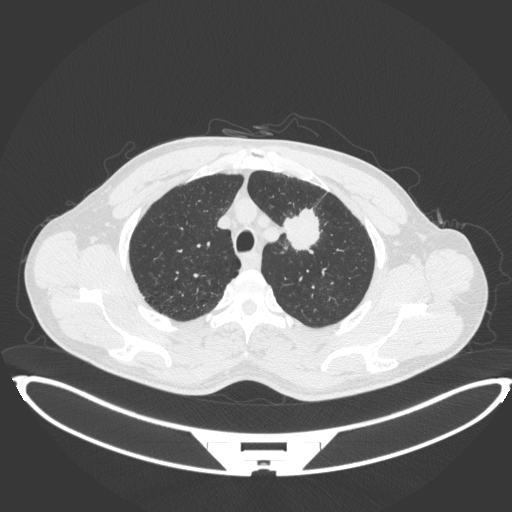
Chest CT, one axial slice; position 354 of 407 along the scan axis; reconstruction kernel B31f; lung window (W 1500 / L -600 HU); 1 mm slice thickness; 512 × 512 image matrix, field of view 457 × 457 mm. Male patient, age 60 years. Case-level facts recorded for this patient, not image findings: clinical TNM (as recorded): T2a N0 M0; histopathological grade: G1-G2.
Annotated regions visible in this slice (rectangle marked by the reading radiologist):
- lung tumour (recorded histology: squamous cell carcinoma): bounding box [x1, y1, x2, y2] px = [279, 205, 323, 253]